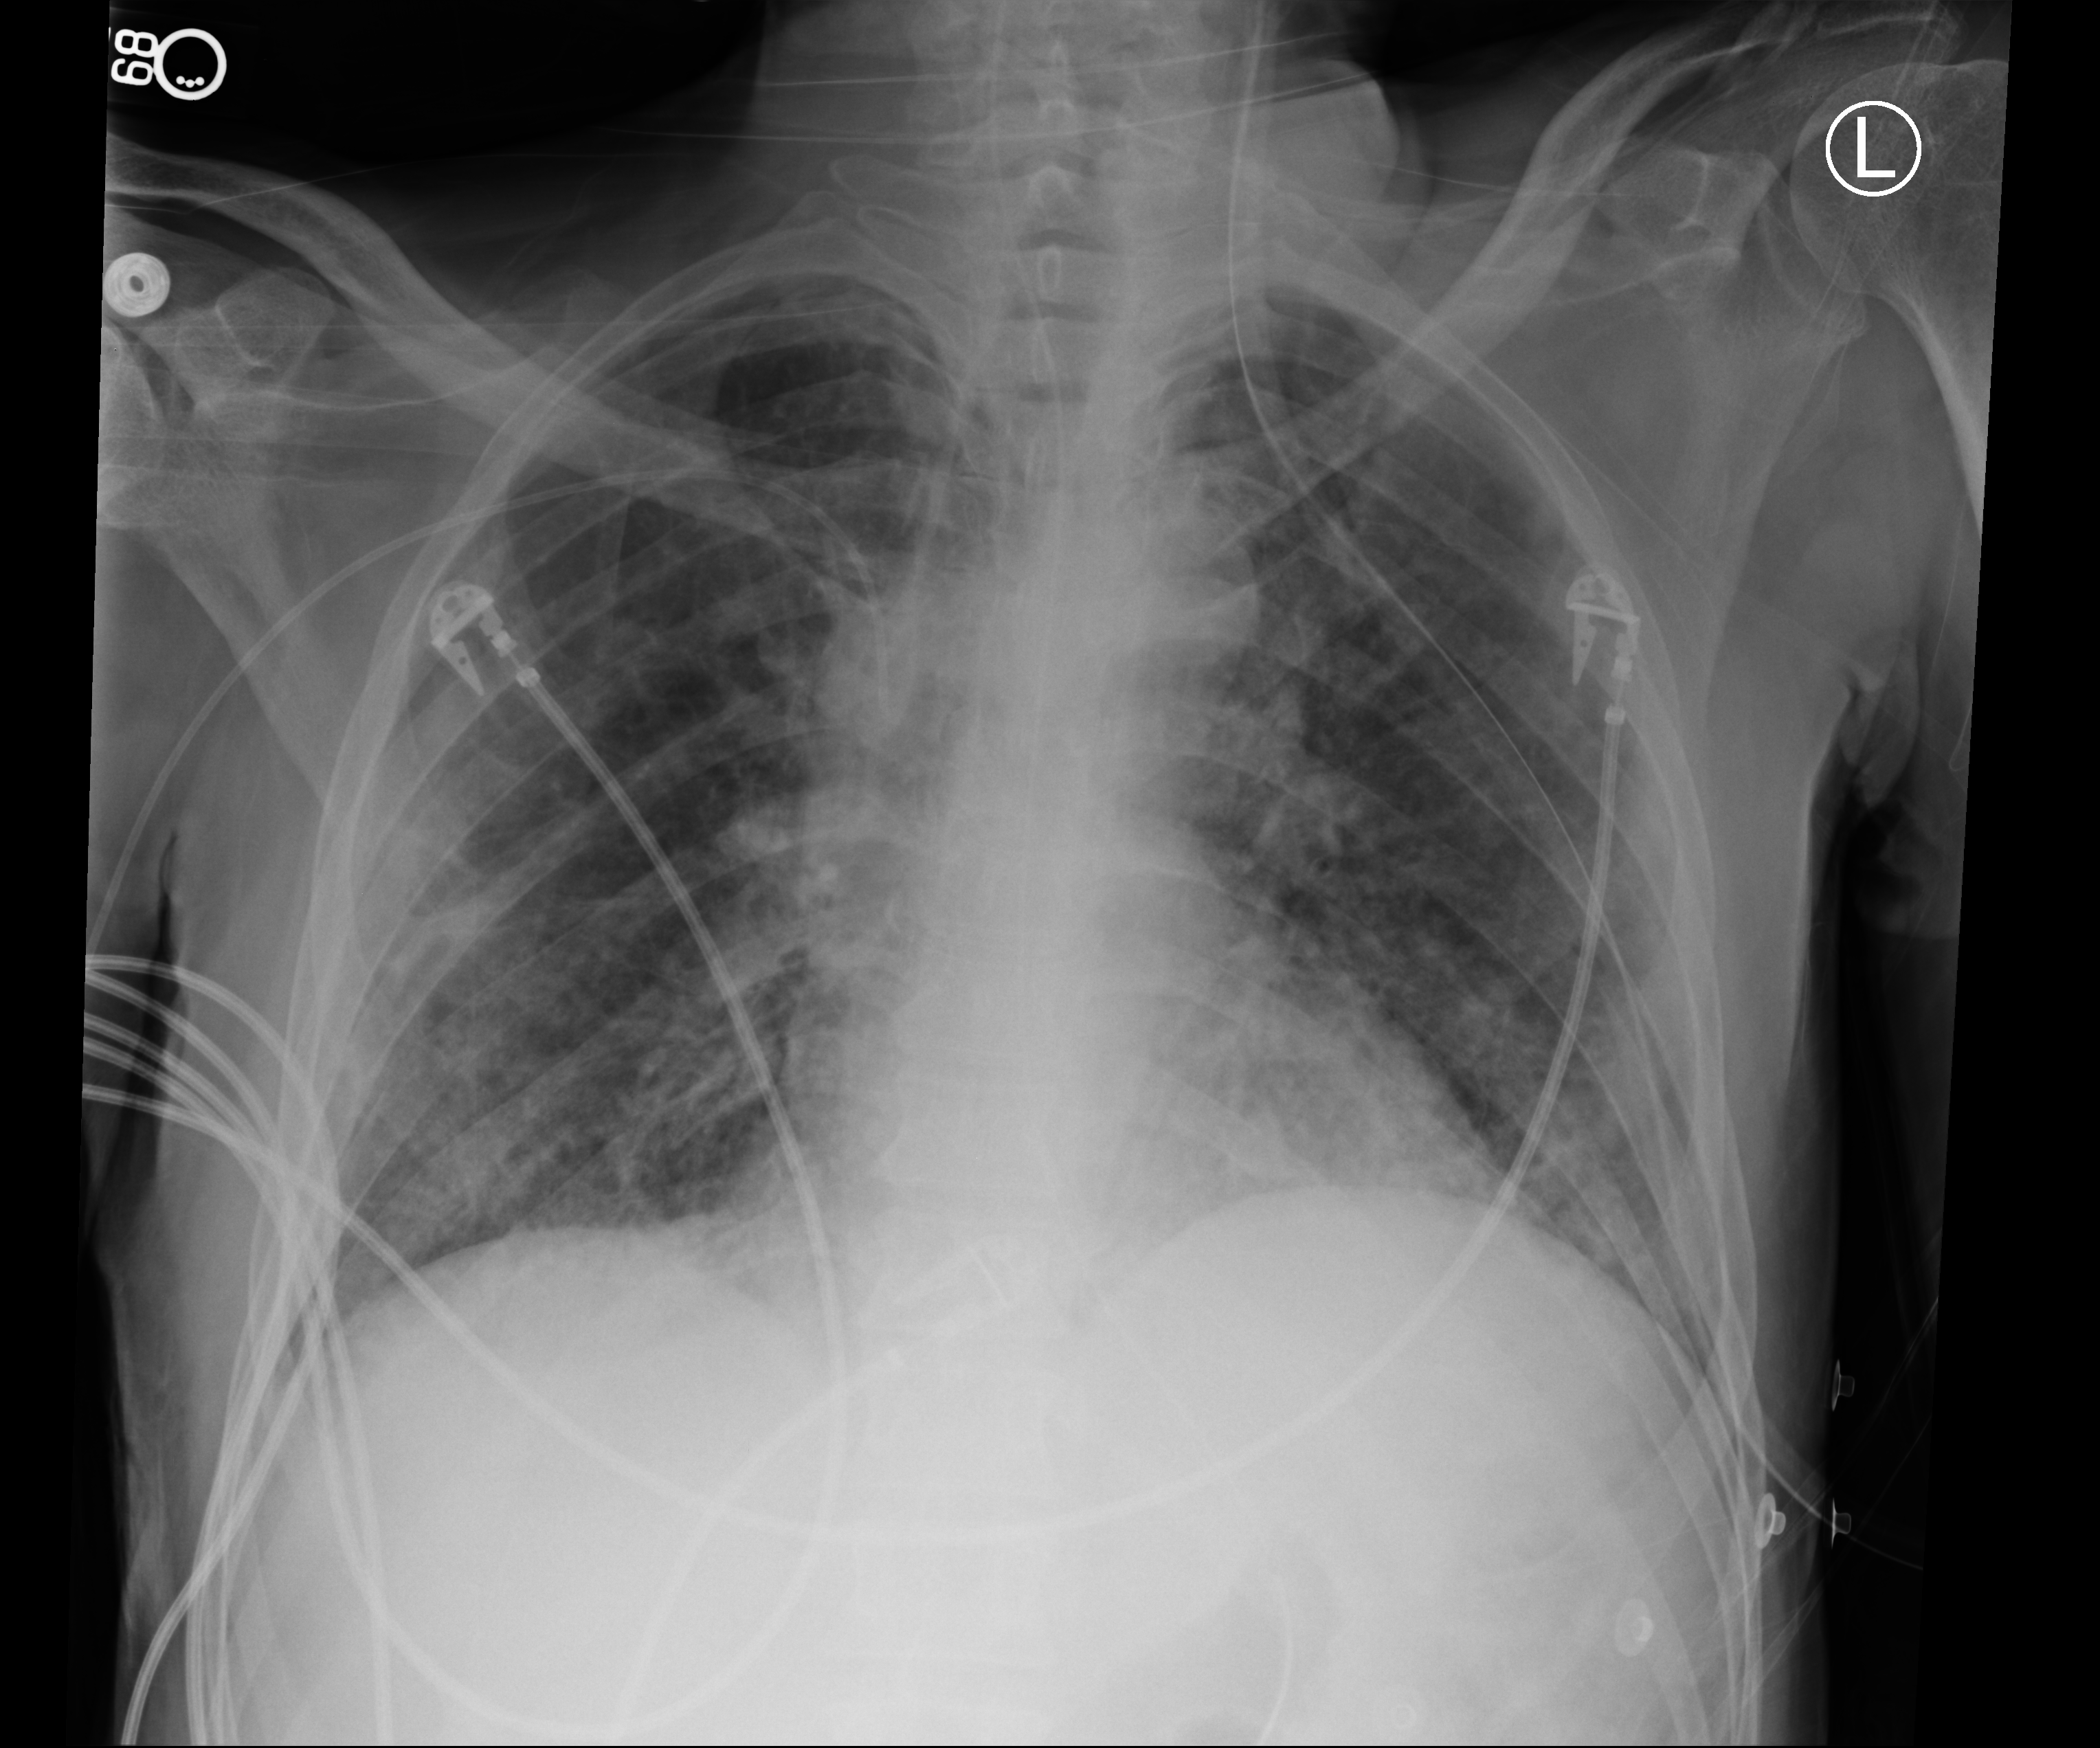
Portable chest radiograph; anteroposterior (AP) projection. Patient hospitalised with COVID-19; male, aged 18–59 years.
From the hospital-stay record, not from the radiograph (when in the stay this image was taken is not recorded): mechanically ventilated during this hospital stay: yes.